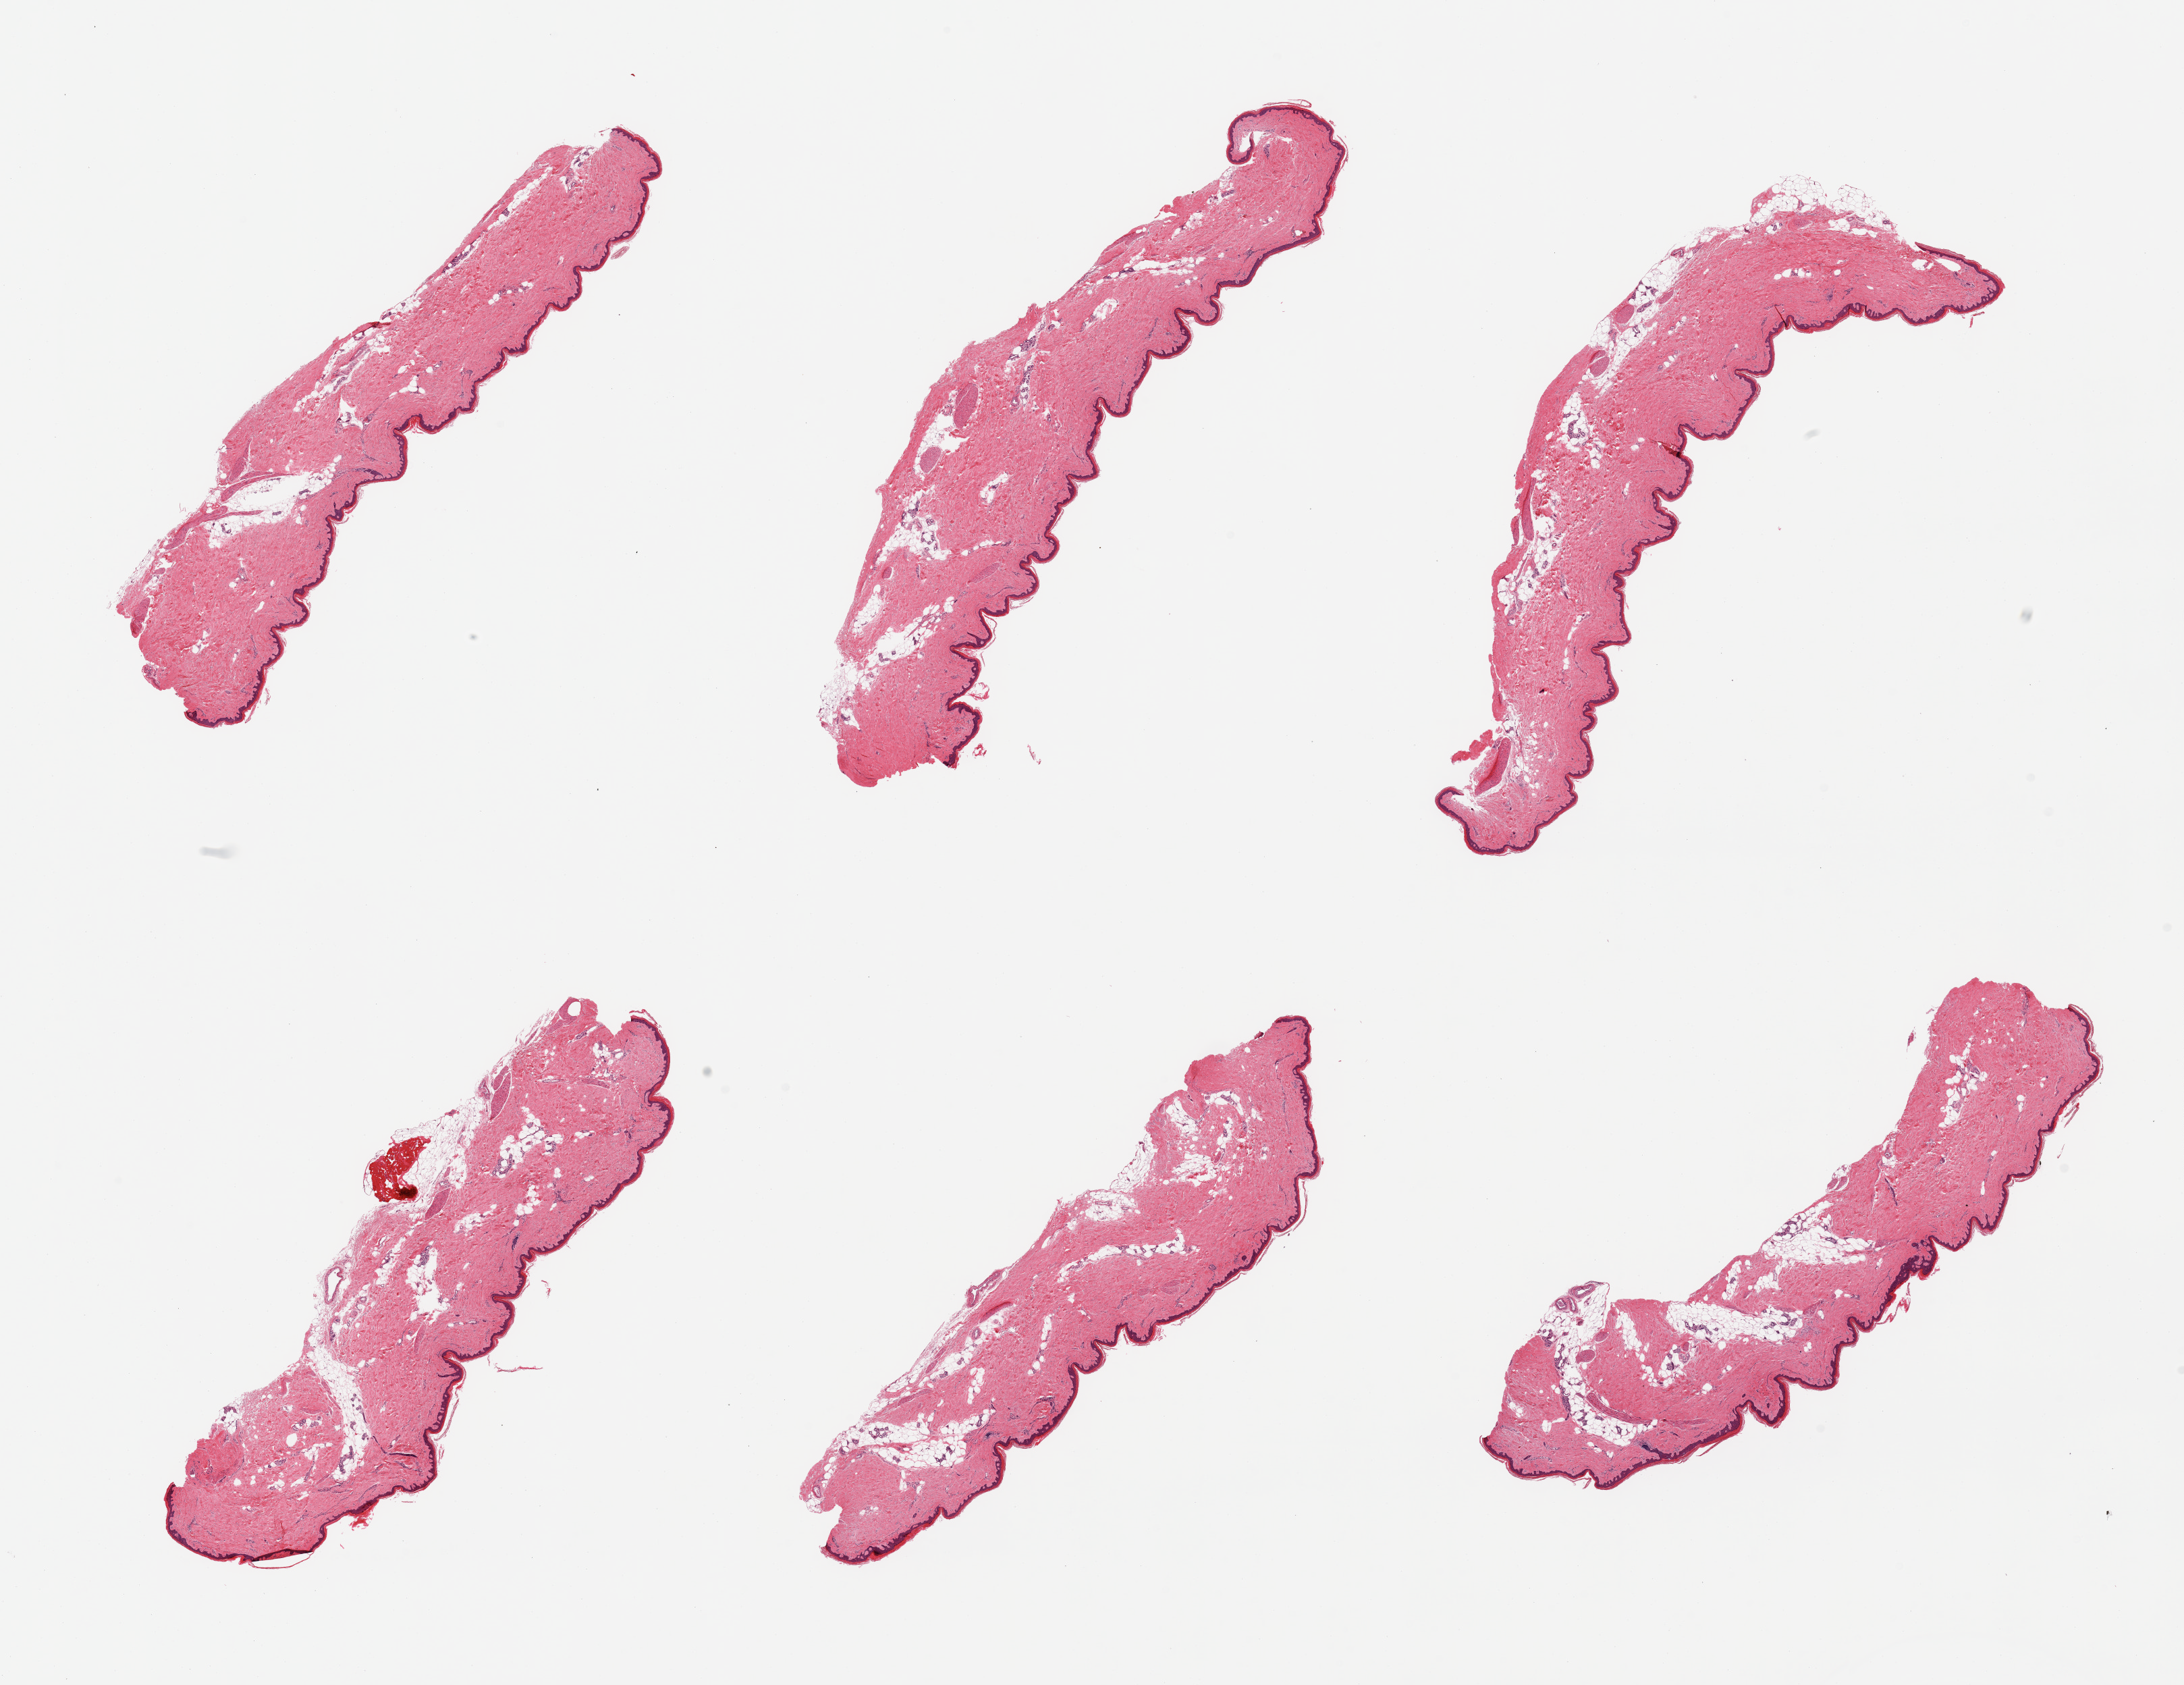
Whole-slide image, haematoxylin and eosin stain — a low-resolution overview of the entire scanned area, about 25.6 x 19.7 mm; PAXgene-fixed paraffin-embedded (PFPE) section; section of skin of lower leg (target tissue); tissue donor sample. Donor sex: female.
* reviewer comment on this tissue sample: 6 pieces, minimal adherent dermal fat; squamous epithelium is ~50microns